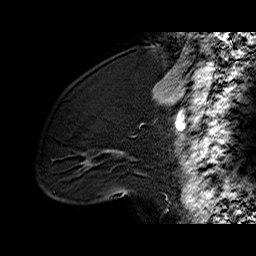
Breast MRI (dynamic contrast-enhanced), one sagittal slice; position 21 of 60 along the scan axis; dynamic contrast-enhanced series, time point 2 of 6 at this slice position (early post-contrast); 1.5 T; TE 6.2 ms, TR 32.4 ms; 4 mm slice thickness; 256 × 256 image matrix. Female patient. From the clinical record (not read from this slice): setting: breast cancer imaged before/during neoadjuvant chemotherapy; receptor status: triple-negative.
Annotated regions visible in this slice (semi-automatically segmented with operator editing):
- analysis volume of interest (the breast-tissue region the enhancement analysis was run in; not a lesion): bounding box <46,98,134,196> (left, top, right, bottom; pixels)
- tumour enhancement mask (voxels above the 100 % enhancement threshold inside the analysis volume of interest): <103,150,124,155>